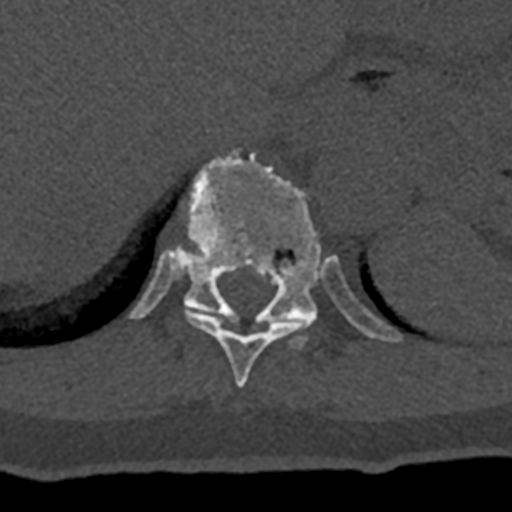
CT including the spine, one axial slice. Position 575 of 797 along the scan axis. Reconstruction kernel Br40s/3. 120 kVp. Bone window (W 1800 / L 400 HU). 512 × 512 image matrix, field of view 160 × 160 mm. Male patient, age 74 years. Case-level facts recorded for this patient, not image findings: primary cancer: renal; vertebrae with lytic lesions (as recorded): T10, L1, L2, L3, L4, L5.
Outlined on this slice (semi-automatically segmented with operator editing):
- T10 vertebra: box from (x=185, y=308) to (x=312, y=387) px
- T11 vertebra: (x=130, y=150)–(x=402, y=349)